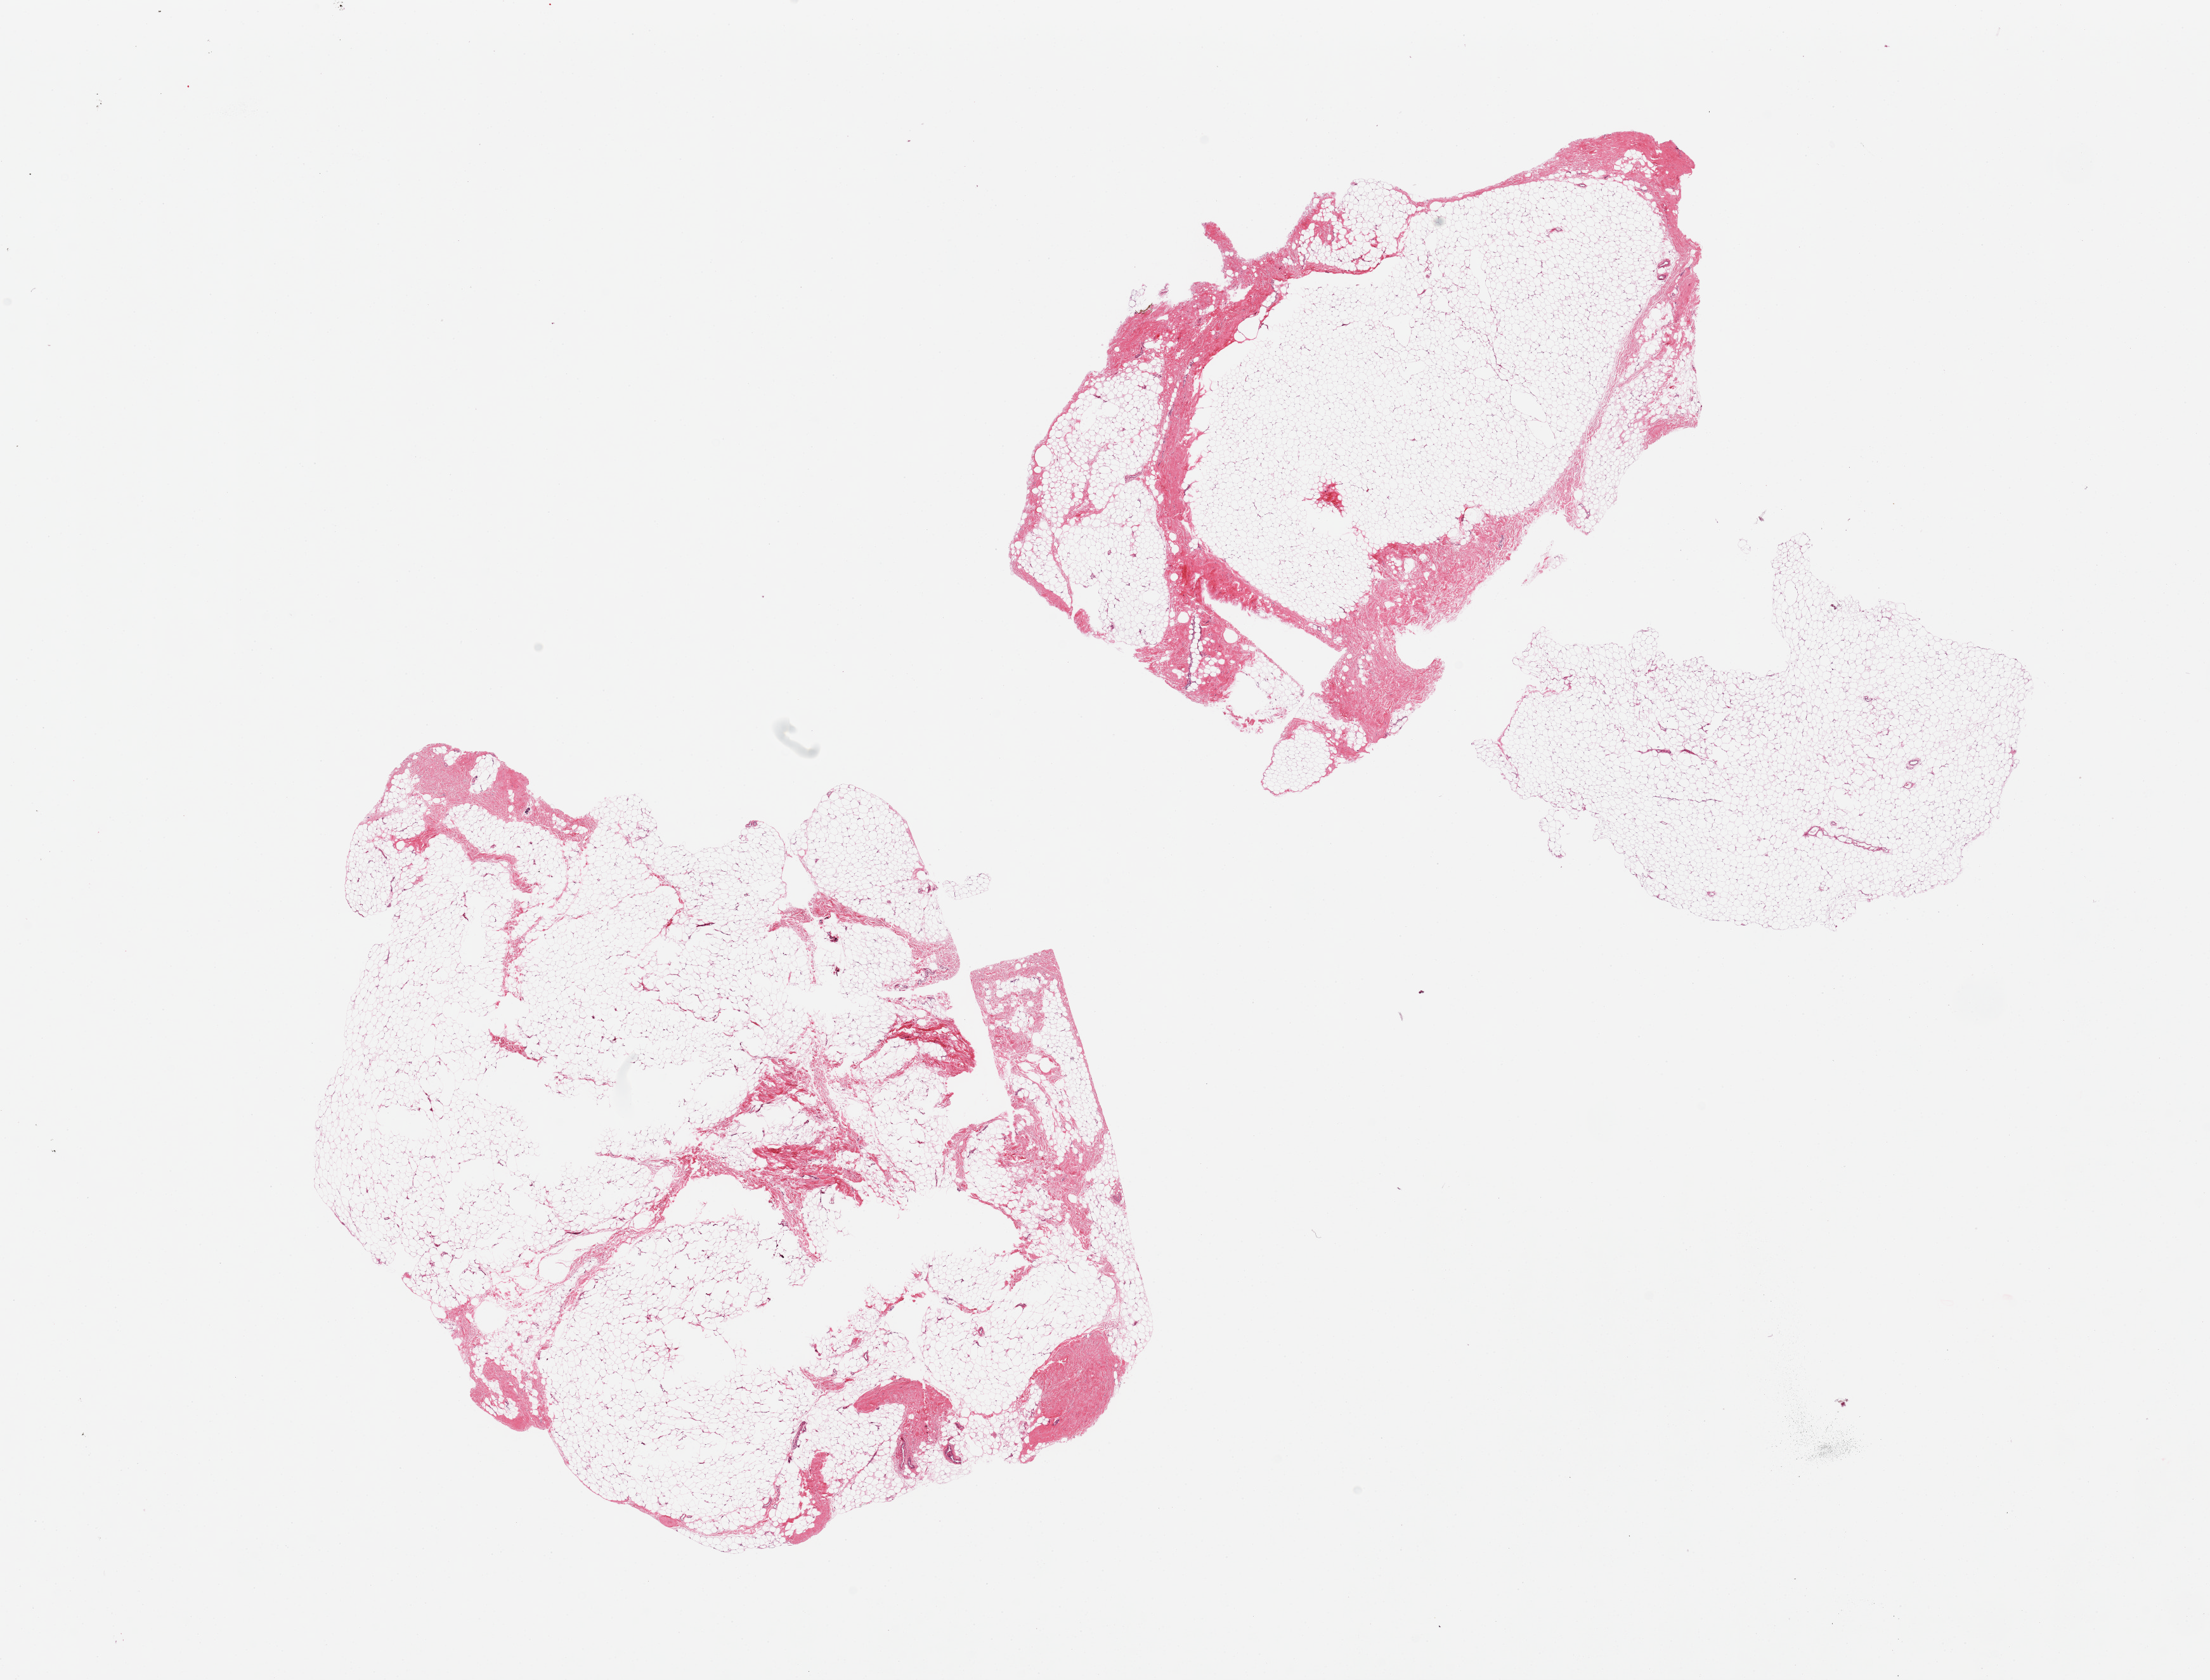
Whole-slide image, haematoxylin and eosin stain, brightfield — shown as a low-resolution overview of the whole scanned area (about 27.6 x 21.0 mm); PAXgene-fixed, paraffin-embedded tissue; sampled site (target tissue): breast; donor tissue sample.
Pathologist's review note for this sample: 2 pieces, no ductal elements, all fibroadipose tissue.